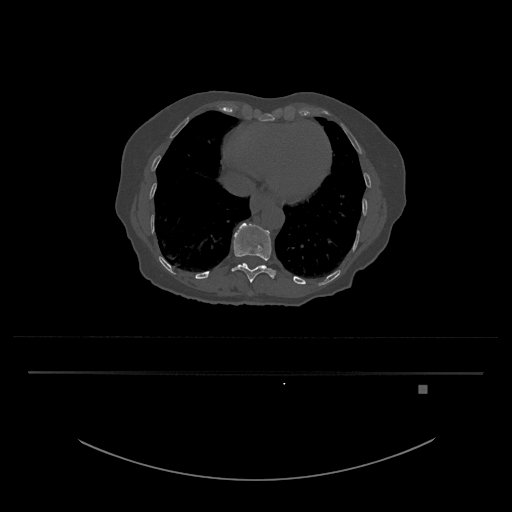
CT including the spine, one axial slice. Reconstruction kernel Br40s/3. 120 kVp. Bone window (W 1800 / L 400 HU). 512 × 512 image matrix, field of view 500 × 500 mm. Female patient, age 57 years. Case-level facts recorded for this patient, not image findings: primary cancer: cervical.
Annotated regions visible in this slice (semi-automatically segmented with operator editing):
- T11 vertebra: bounding box (x1, y1, x2, y2) in pixels: (232, 223, 276, 283)
- T12 vertebra: (239, 263, 265, 266)